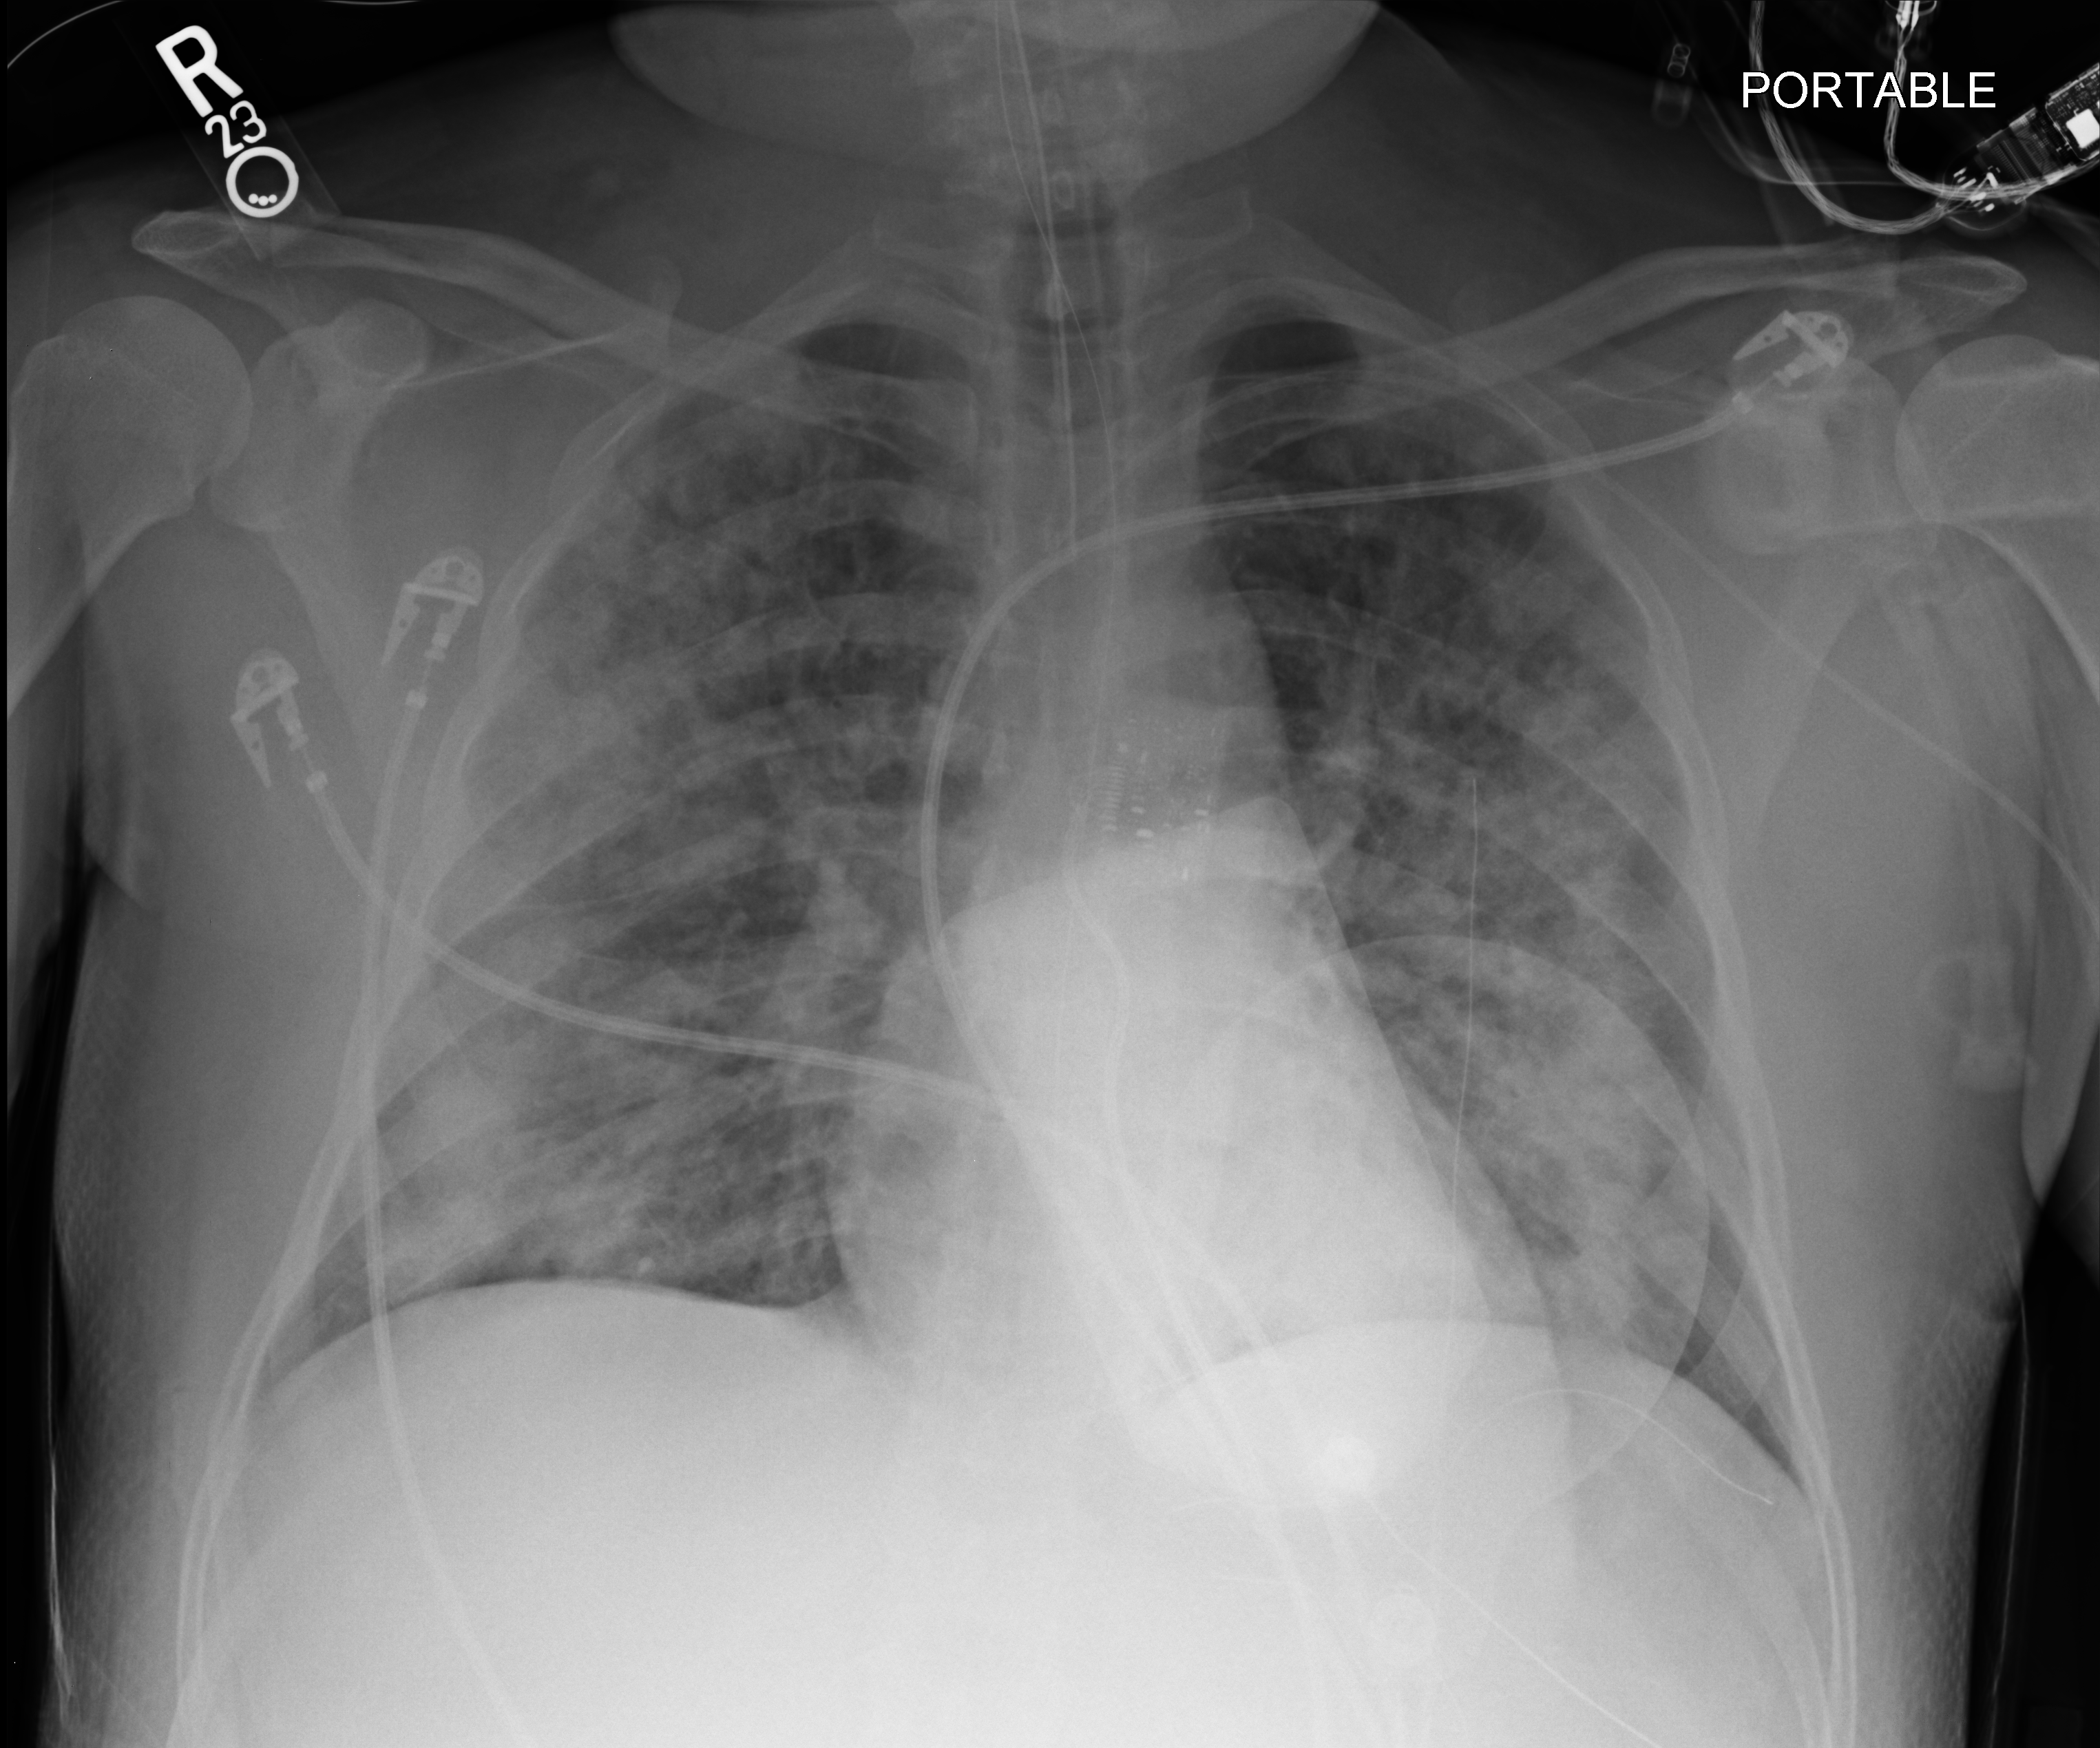
Chest X-ray (portable), anteroposterior (AP) projection. Patient hospitalised with COVID-19, aged 18–59 years.
From the hospital-stay record, not from the radiograph (when in the stay this image was taken is not recorded):
- mechanically ventilated during this hospital stay: yes
- admitted to intensive care during this hospital stay: no